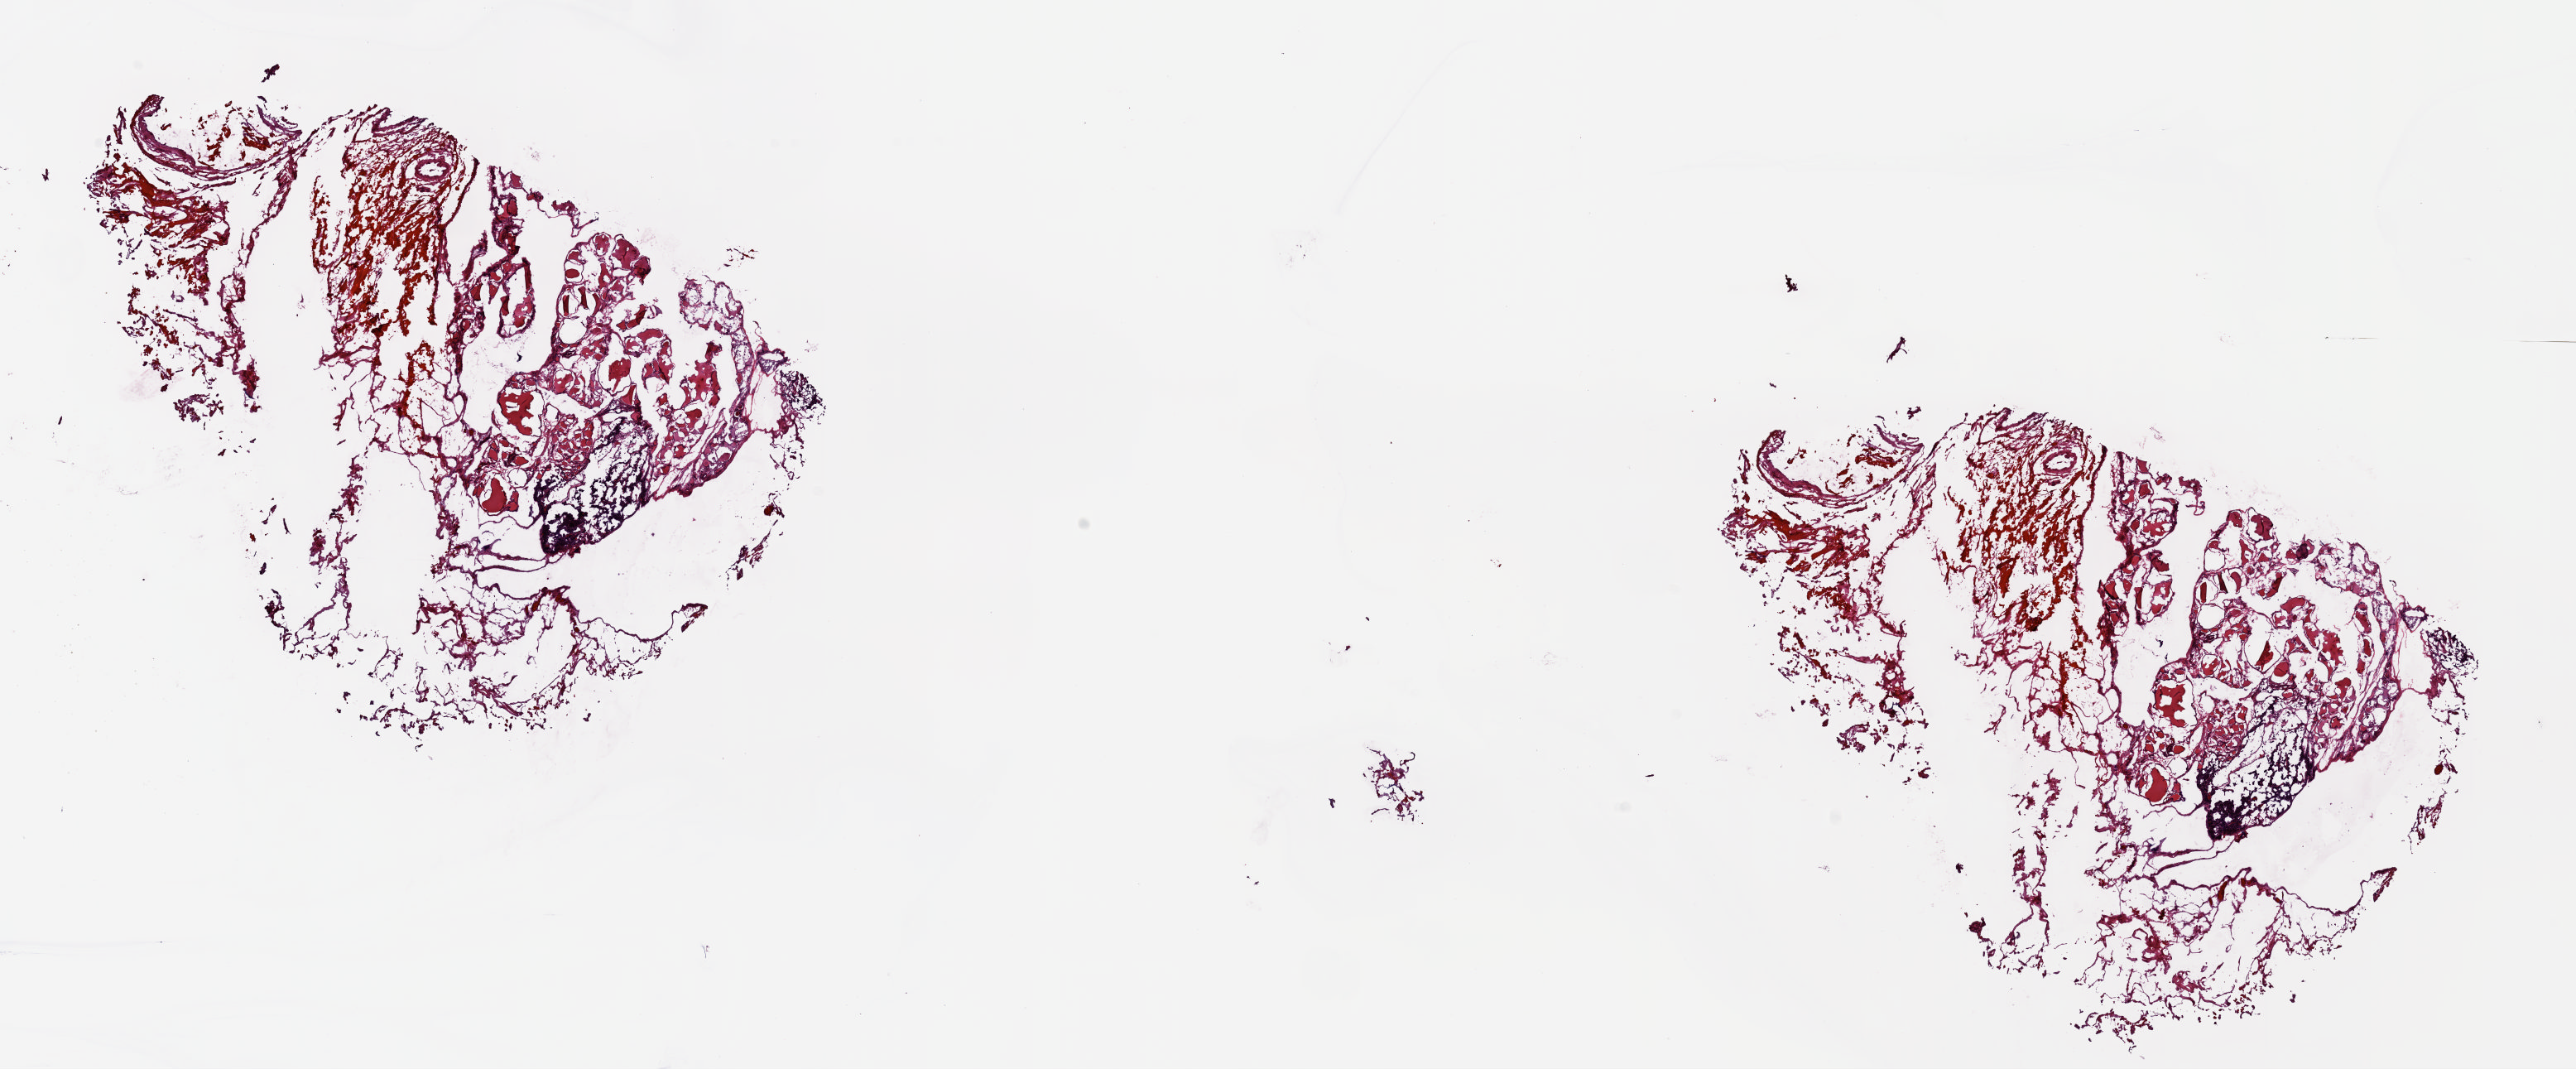
H&E-stained whole-slide image, shown as a low-resolution overview of the whole scanned area (about 24.5 x 10.2 mm, acquisition: 20x scan). Frozen section from the top of the tissue portion. Solid tissue normal (non-tumour tissue) sample from the thyroid. Female, age 41 years at initial diagnosis. Composition of this section per pathologist review: tumour cells 0%, tumour nuclei 0%, normal cells 100%, stromal cells 0%, necrosis 0%. Infiltration values recorded for this section: lymphocyte infiltration 8%, monocyte infiltration 1%, neutrophil infiltration 0%.
This section: solid tissue normal sample (biorepository sample class). Patient diagnosis: Papillary adenocarcinoma, NOS (thyroid gland).